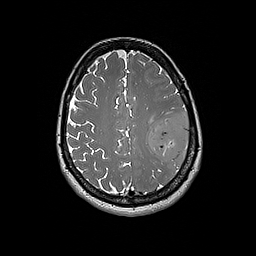
Brain MRI from a brain-tumour surgery series, one axial slice. Position 67 of 192 along the scan axis. 256 × 256 image matrix, field of view 250 × 250 mm. Case-level facts recorded for this patient, not image findings: histopathology: Glioblastoma; WHO grade: 4; IDH mutation: no.
Structures marked on this image (expert manual segmentation):
- tumour: box from (x=148, y=114) to (x=189, y=167) px